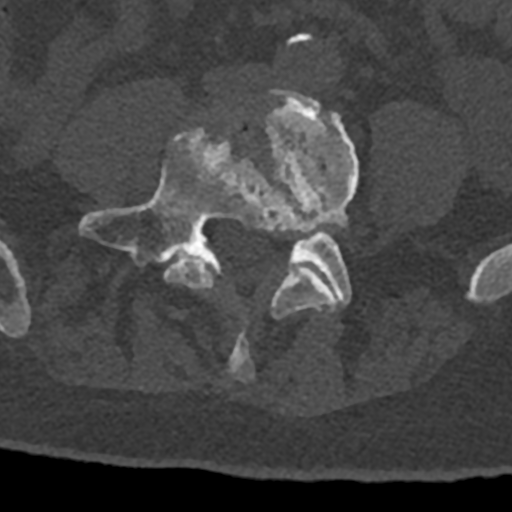
CT including the spine, one axial slice. Position 225 of 797 along the scan axis. Reconstruction kernel Br40s/3. 120 kVp. Bone window (W 1800 / L 400 HU). 512 × 512 image matrix, field of view 160 × 160 mm. Male patient, age 74 years. Case-level facts recorded for this patient, not image findings: primary cancer: renal; vertebrae with lytic lesions (as recorded): T10, L1, L2, L3, L4, L5.
Annotated regions visible in this slice (semi-automatically segmented with operator editing):
- L4 vertebra: box from (x=164, y=90) to (x=359, y=382) px
- L5 vertebra: (x=79, y=130)–(x=352, y=305)